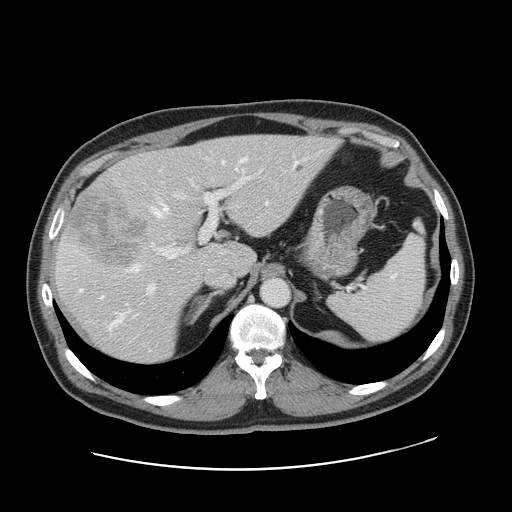
Contrast-enhanced abdominal CT, one axial slice. Position 114 of 178 along the scan axis. Intravenous contrast given. Soft-tissue window (W 400 / L 40 HU). 512 × 512 image matrix, field of view 403 × 403 mm. Male patient, age 63 years. Case-level facts recorded for this patient, not image findings: diagnosis: colorectal cancer liver metastases, imaged before liver resection; multiple liver metastases: yes.
Structures marked on this image (expert manual segmentation):
- hepatic veins: bounding box (x1, y1, x2, y2) in pixels: (79, 158, 297, 326)
- liver: (54, 136, 336, 365)
- planned liver remnant (the part of the liver to remain after resection): (136, 136, 335, 275)
- portal vein (with intrahepatic branches): (147, 170, 262, 293)
- liver metastasis: (297, 166, 303, 172)
- liver metastasis: (70, 192, 149, 270)